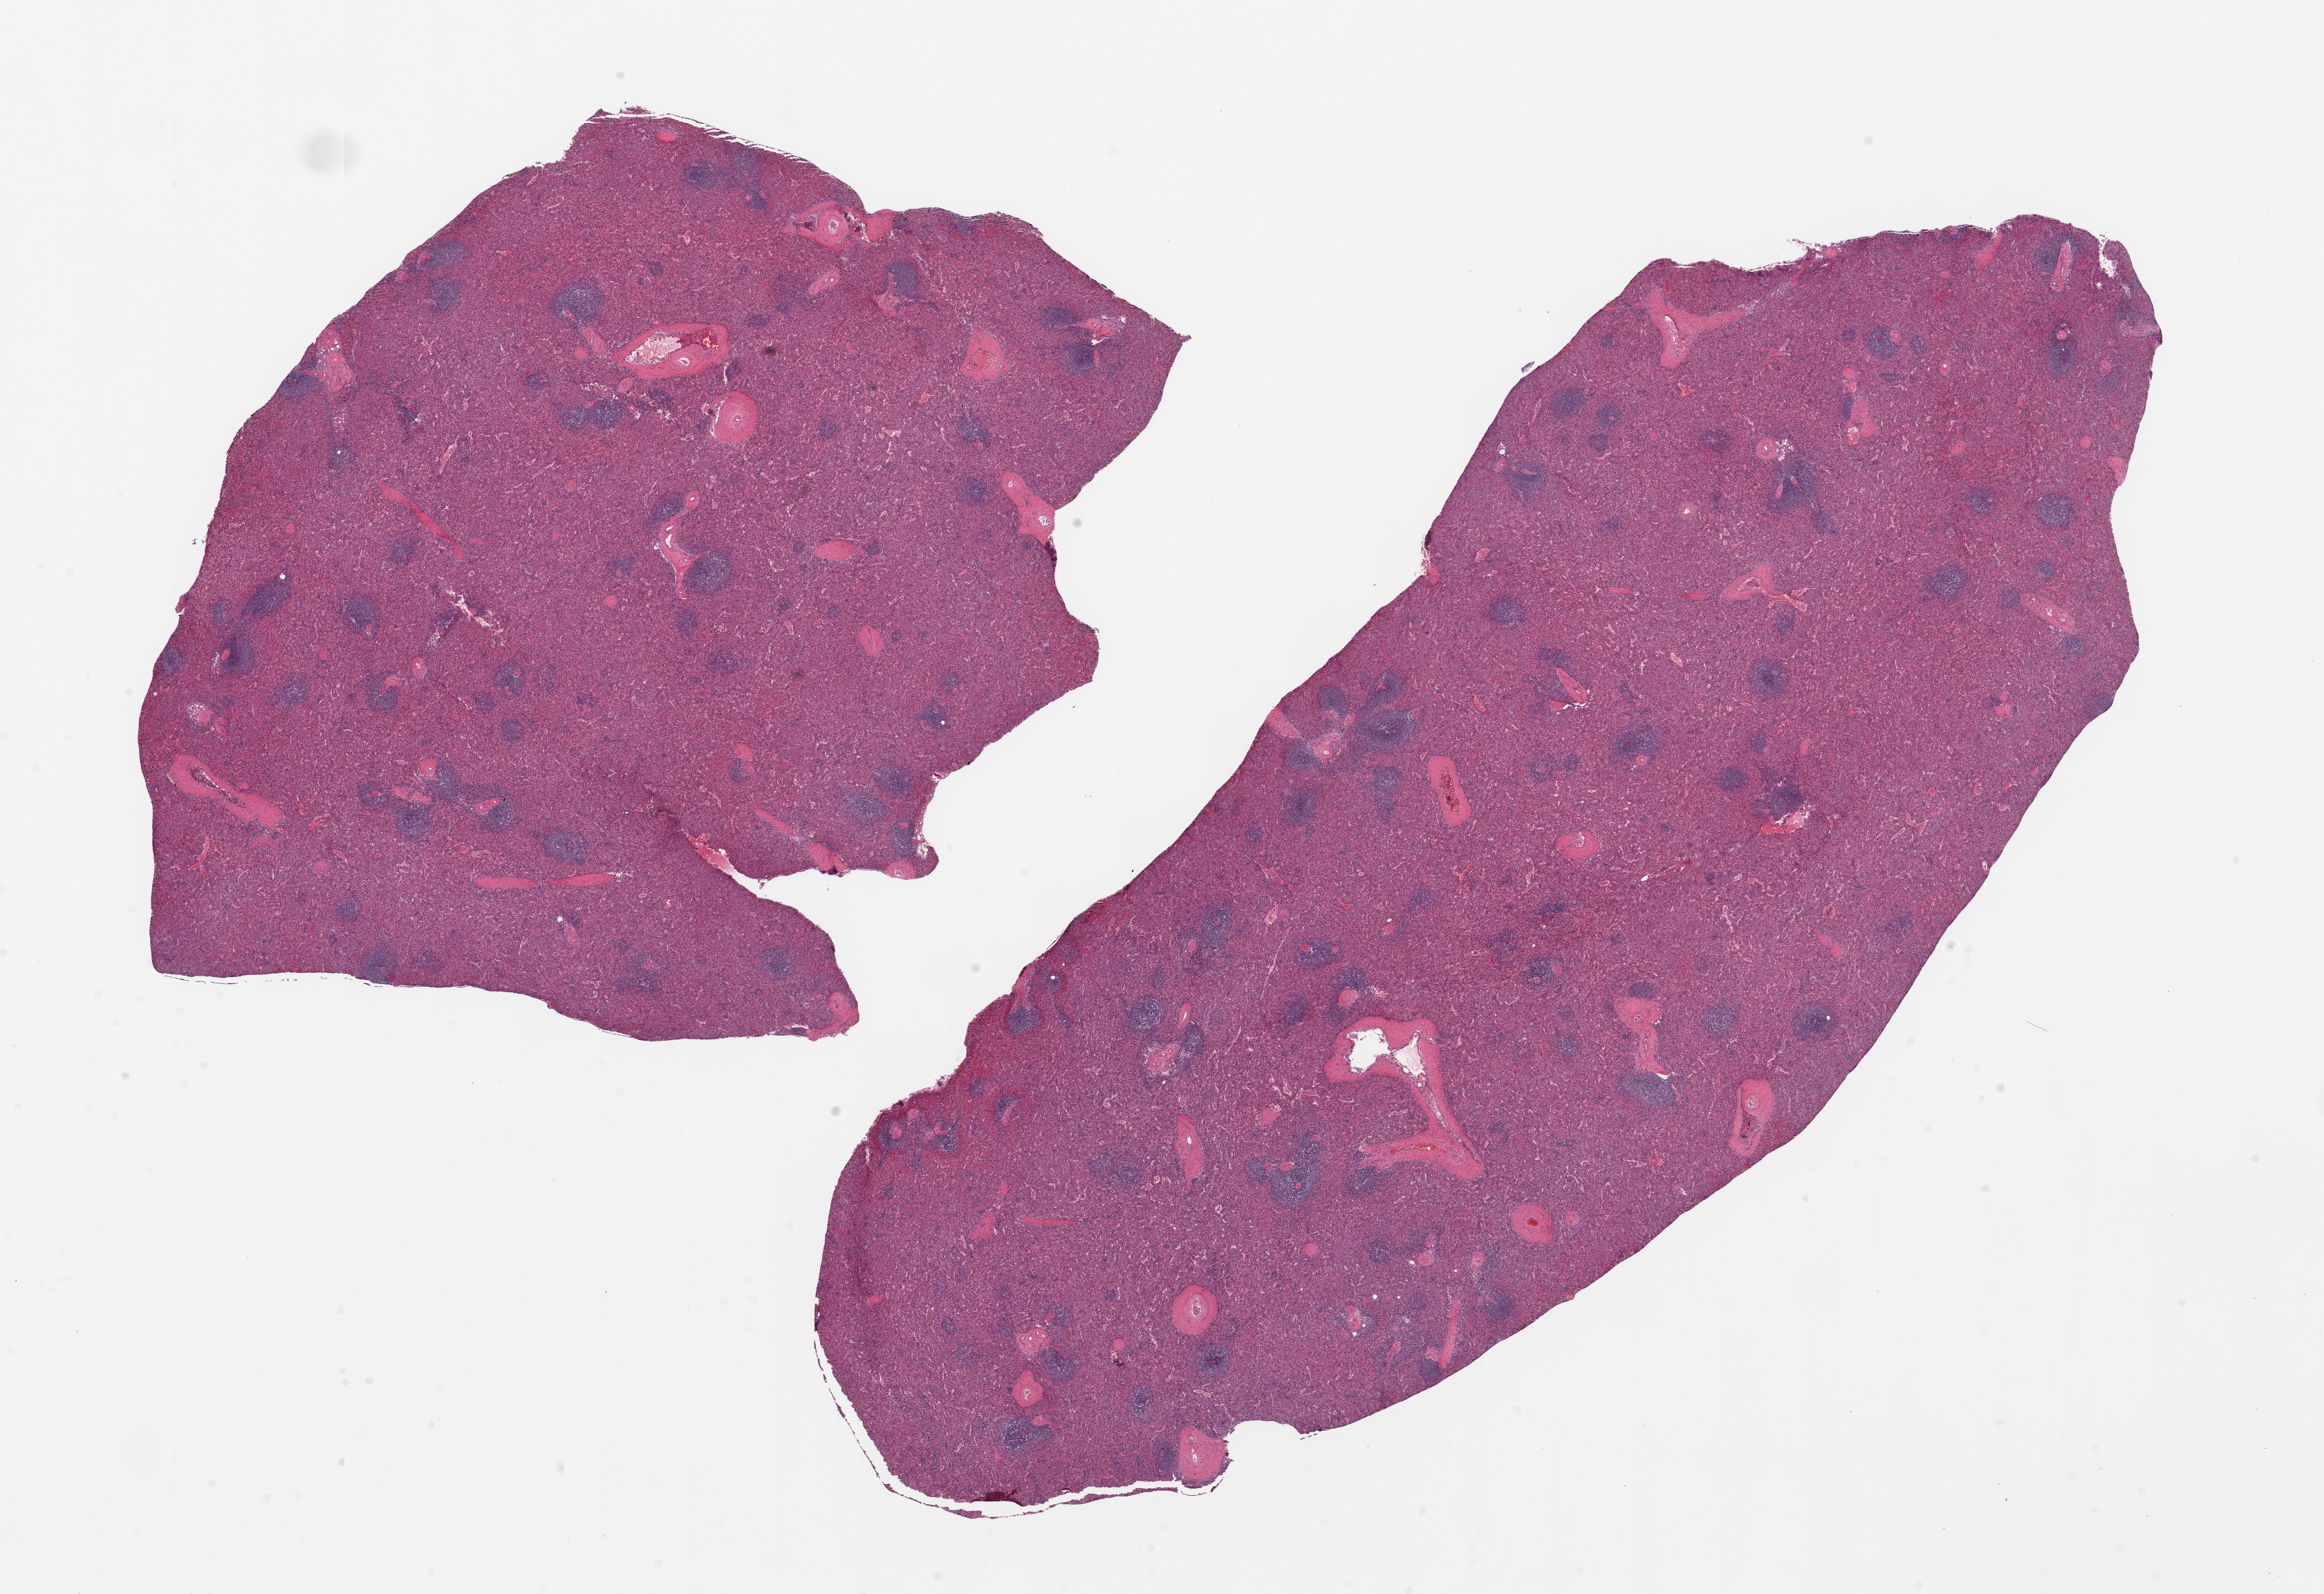
Digitized hematoxylin and eosin (H&E)-stained section — whole scanned area (about 26.6 x 18.2 mm, acquisition: 20x scan) shown as a low-resolution overview. PAXgene-fixed, paraffin-embedded tissue. Target tissue: spleen. Tissue donor sample. Donor: male.
- review note (as recorded): 2 pieces